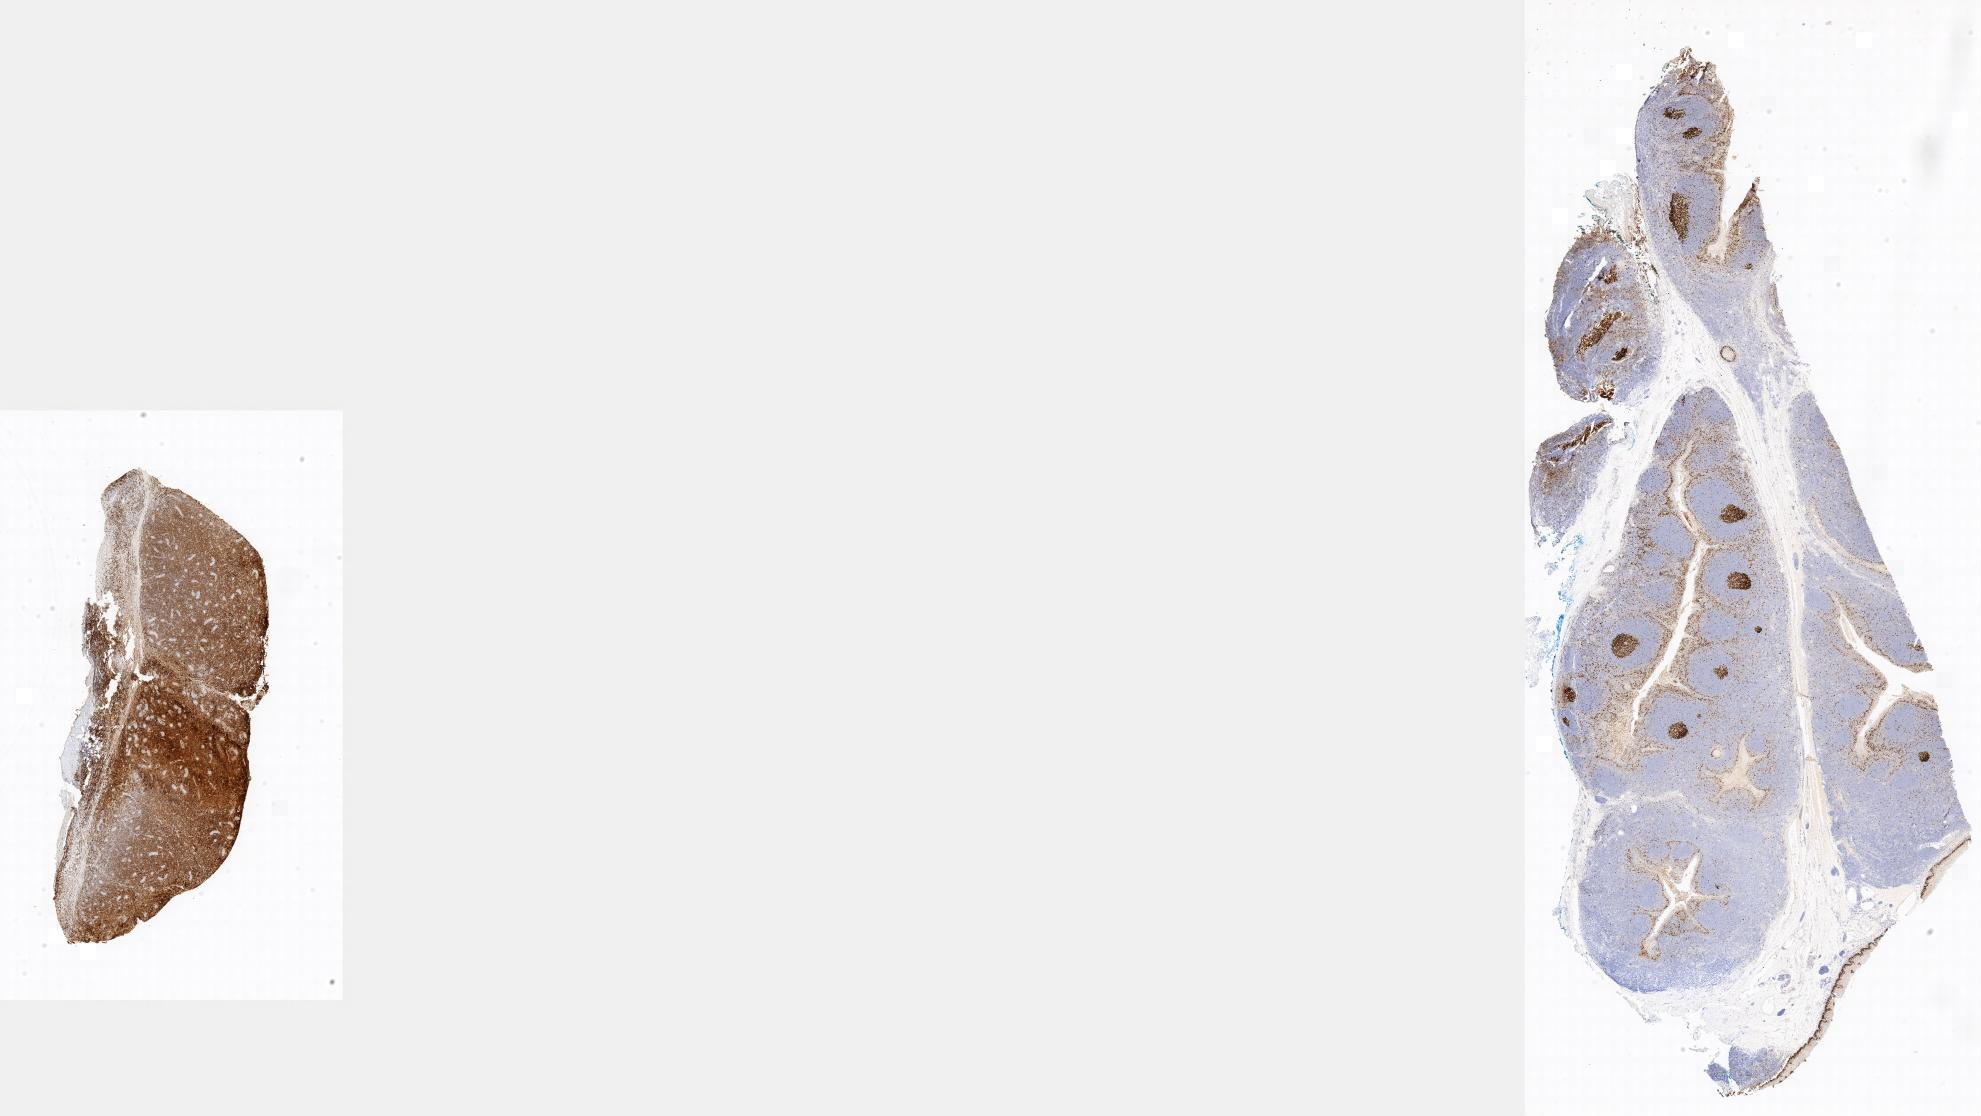
Immunohistochemistry (IHC) whole-slide image stained for Ki-67 — whole scanned area shown as a low-resolution overview; tumor tissue; site: testis. Male patient; age at initial diagnosis 8 years.
Histologic diagnosis: Burkitt lymphoma, NOS.